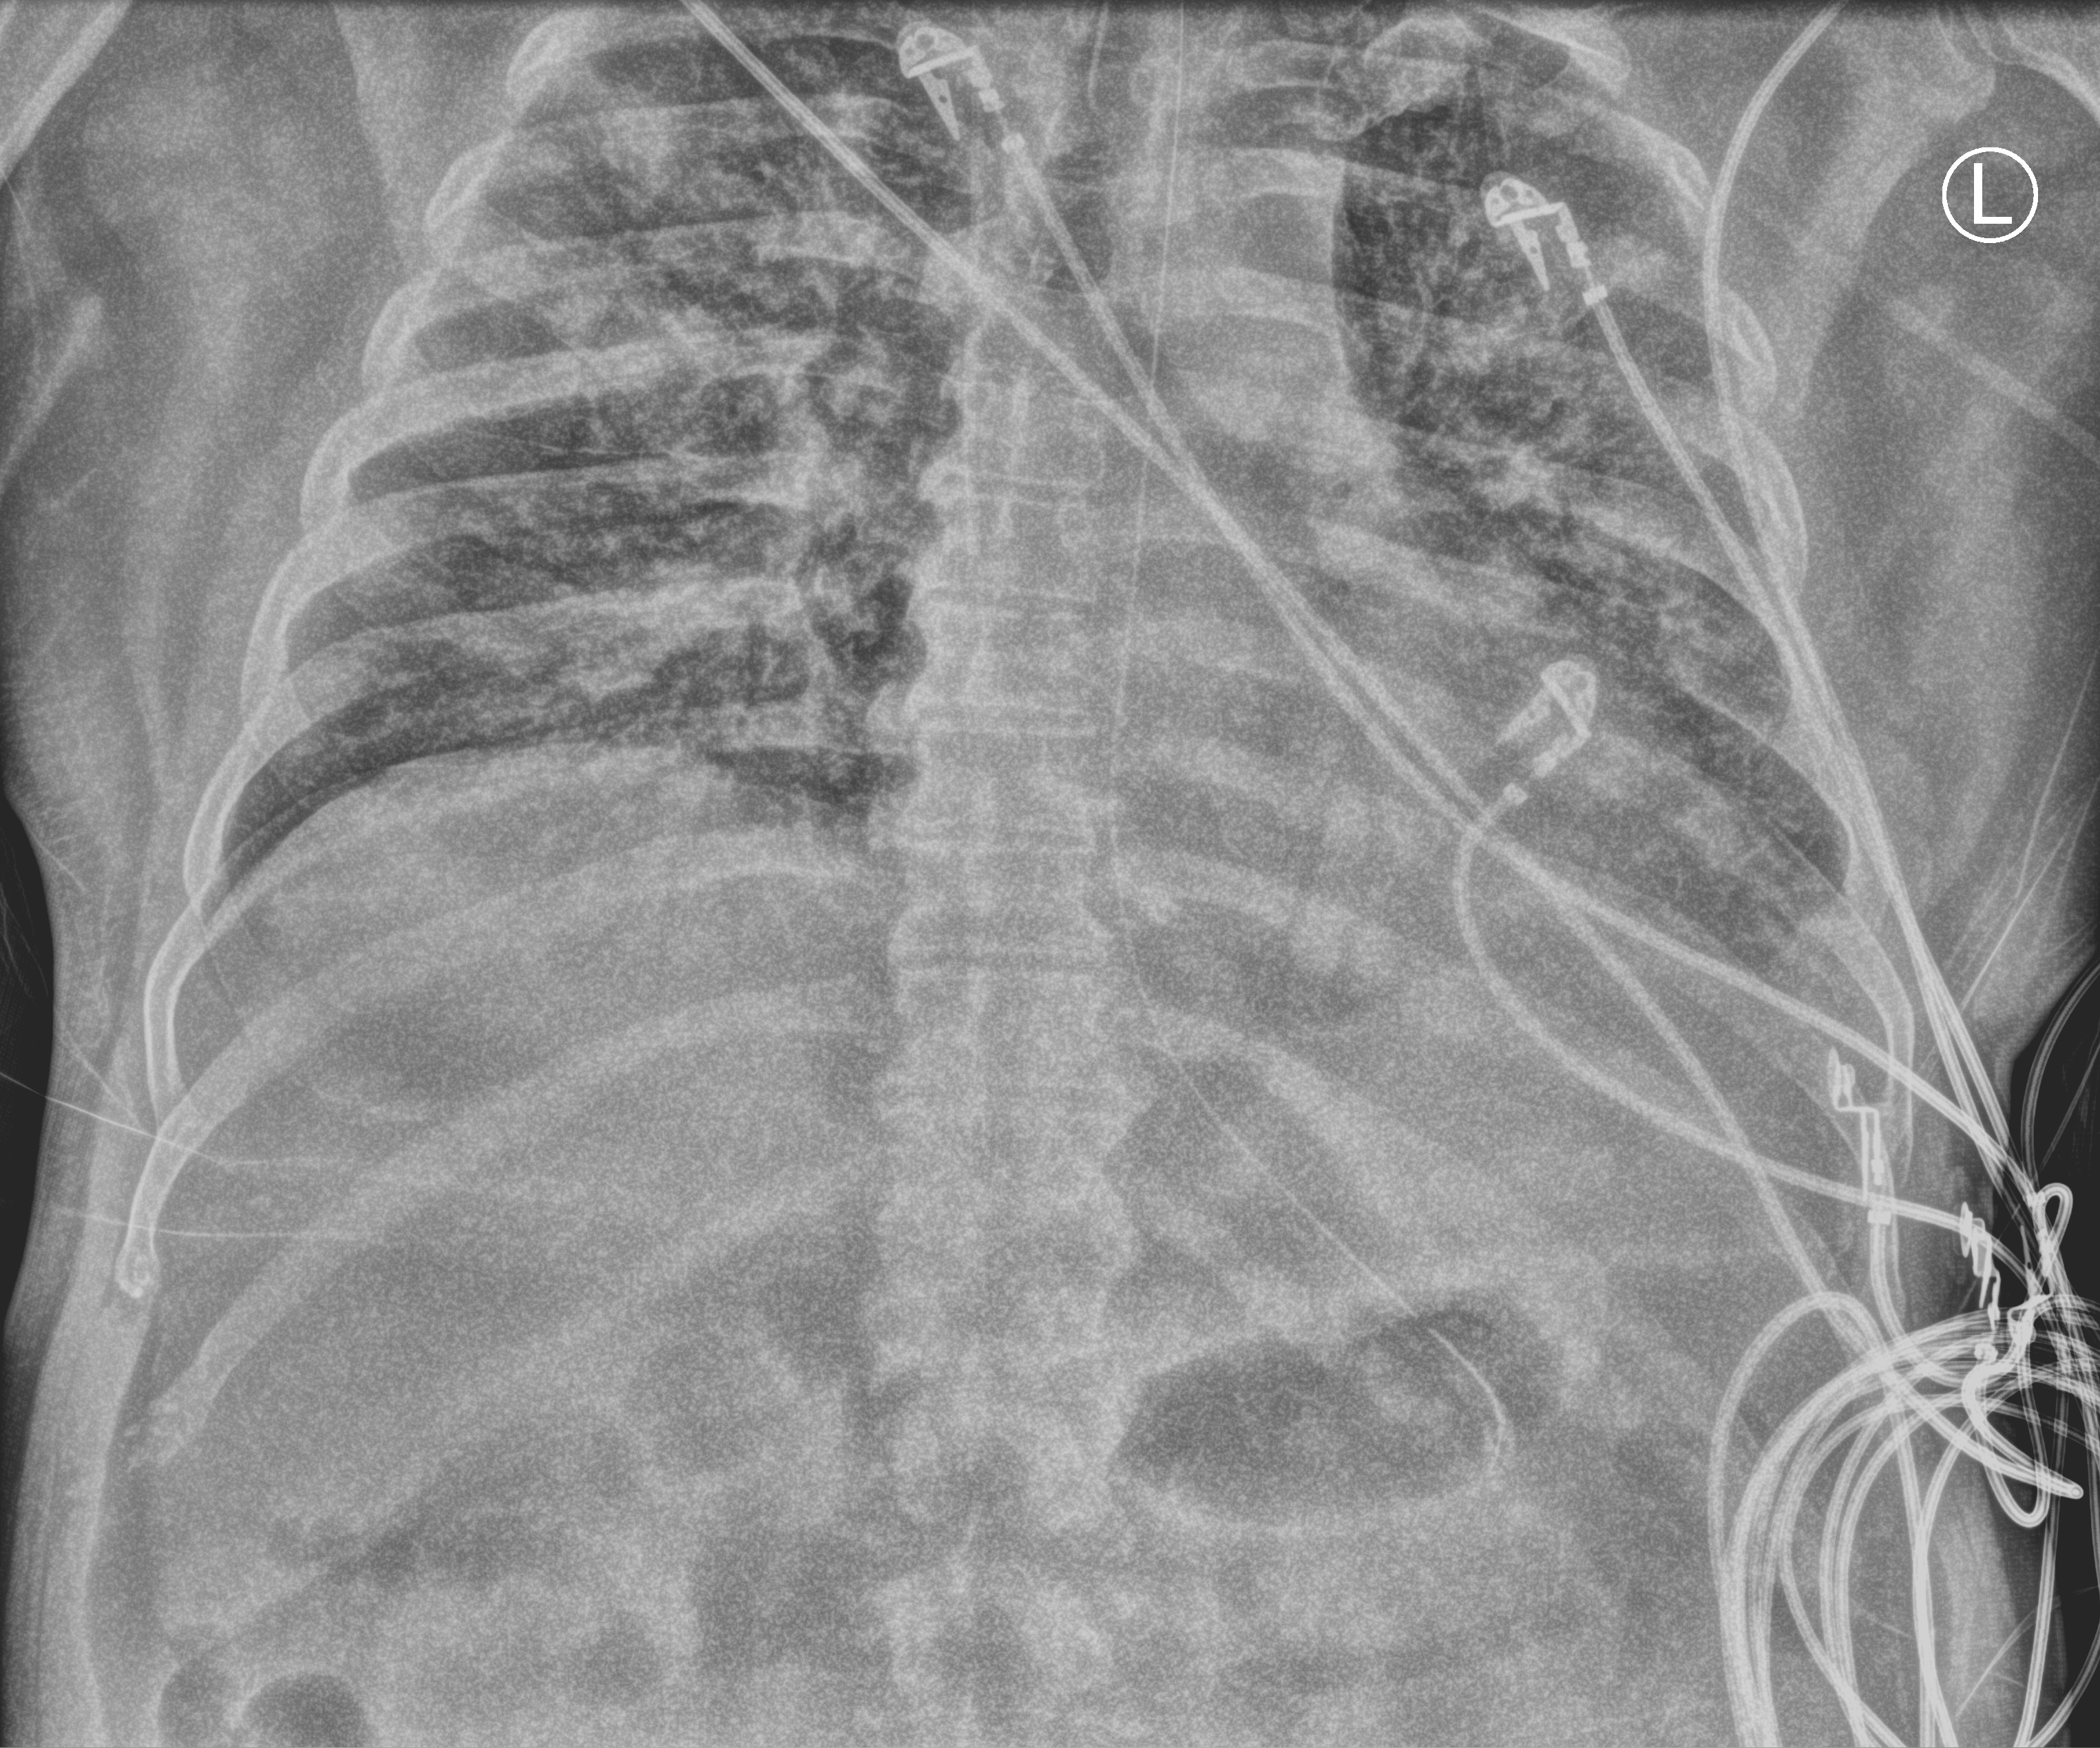
Portable chest radiograph; anteroposterior (AP) projection. Patient hospitalised with COVID-19; male, aged 18–59 years.
From the hospital-stay record, not from the radiograph (when in the stay this image was taken is not recorded):
- length of hospital stay: 26 days
- mechanically ventilated during this hospital stay: yes
- COPD (admission record): no